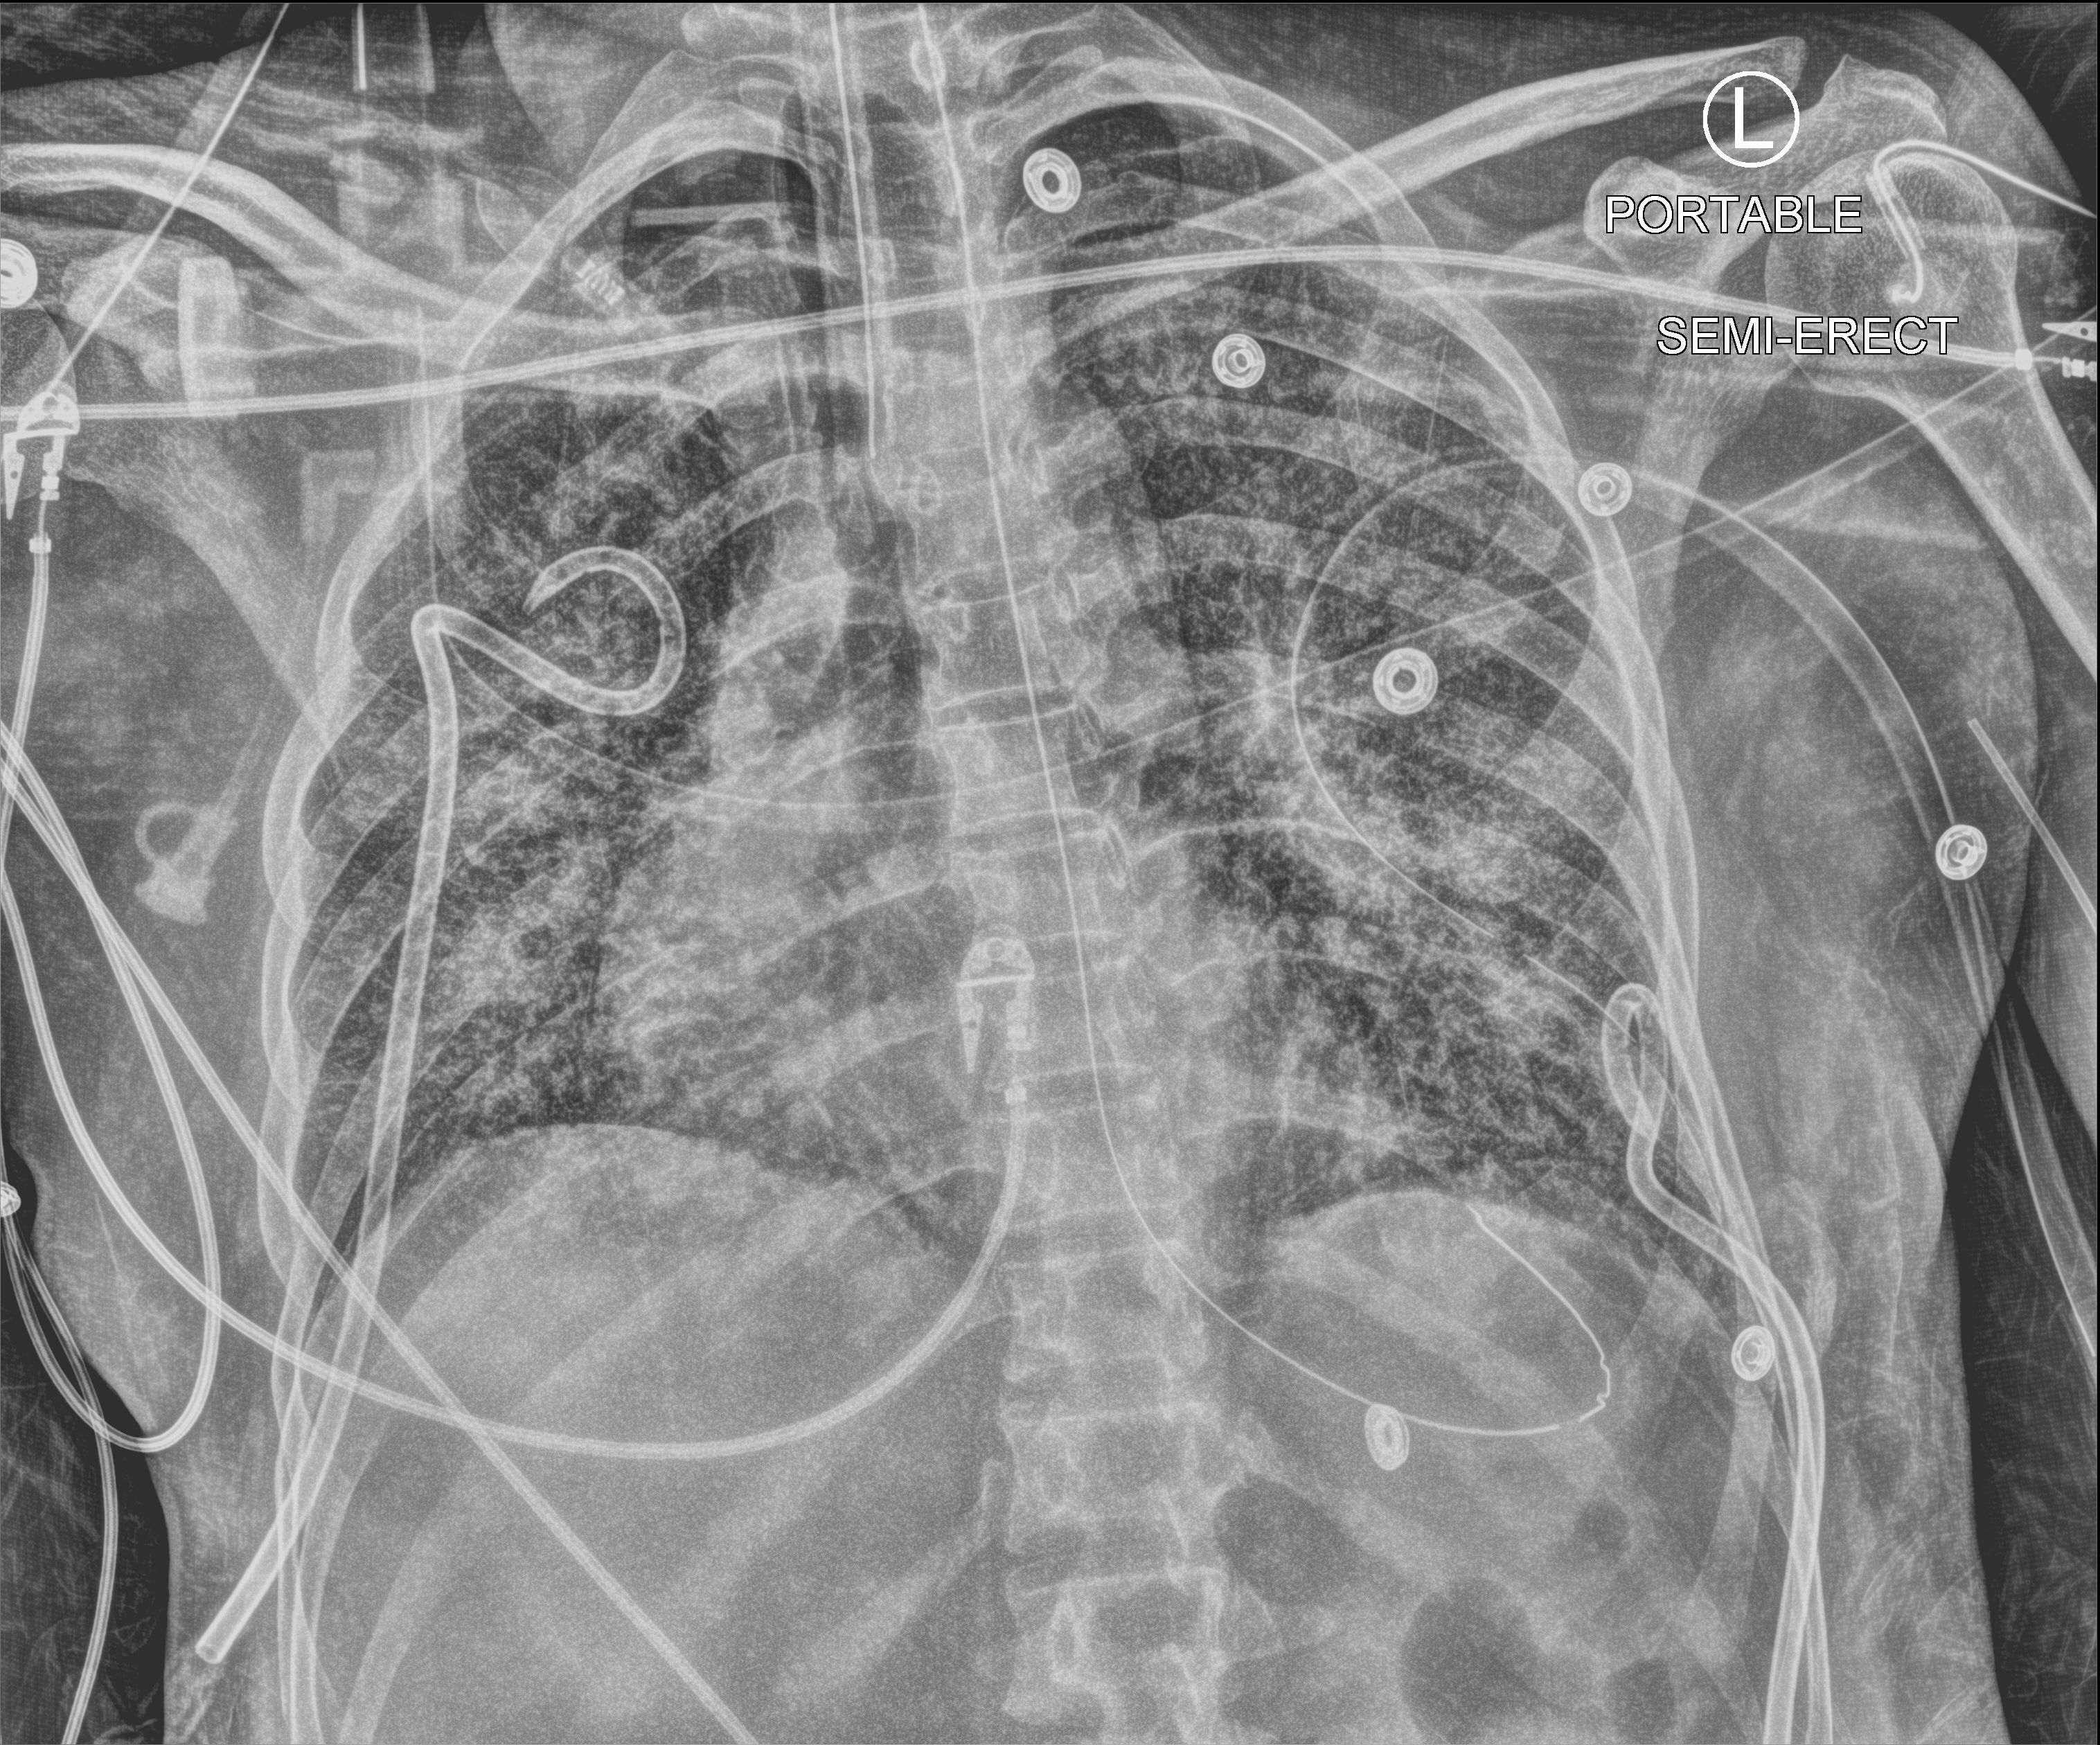
Bedside chest radiograph (computed radiography), anteroposterior (AP) projection. Patient hospitalised with COVID-19, aged 18–59 years.
From the hospital-stay record, not from the radiograph (when in the stay this image was taken is not recorded): admitted to intensive care during this hospital stay: yes.